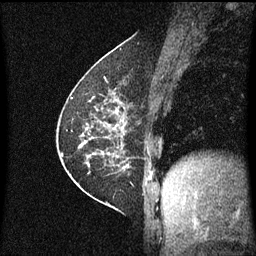
Breast MRI (dynamic contrast-enhanced), one sagittal slice. Slice 26 of 60 in the series (ordered by position). Dynamic contrast-enhanced series, image 2 of 3 at this slice position (ordered by acquisition). 1.5 T. TE 4.2 ms, TR 8.4 ms. 2 mm slice thickness. 256 × 256 image matrix. Female patient, age 60 years.
Annotated regions visible in this slice (semi-automatic segmentation, software-assisted and operator-edited):
- analysis volume of interest (the breast-tissue region the enhancement analysis was run in; not a lesion): bounding box <69,66,138,193> (left, top, right, bottom; pixels)
- tumour enhancement mask (voxels above the 70 % enhancement threshold inside the analysis volume of interest): <71,74,129,173>